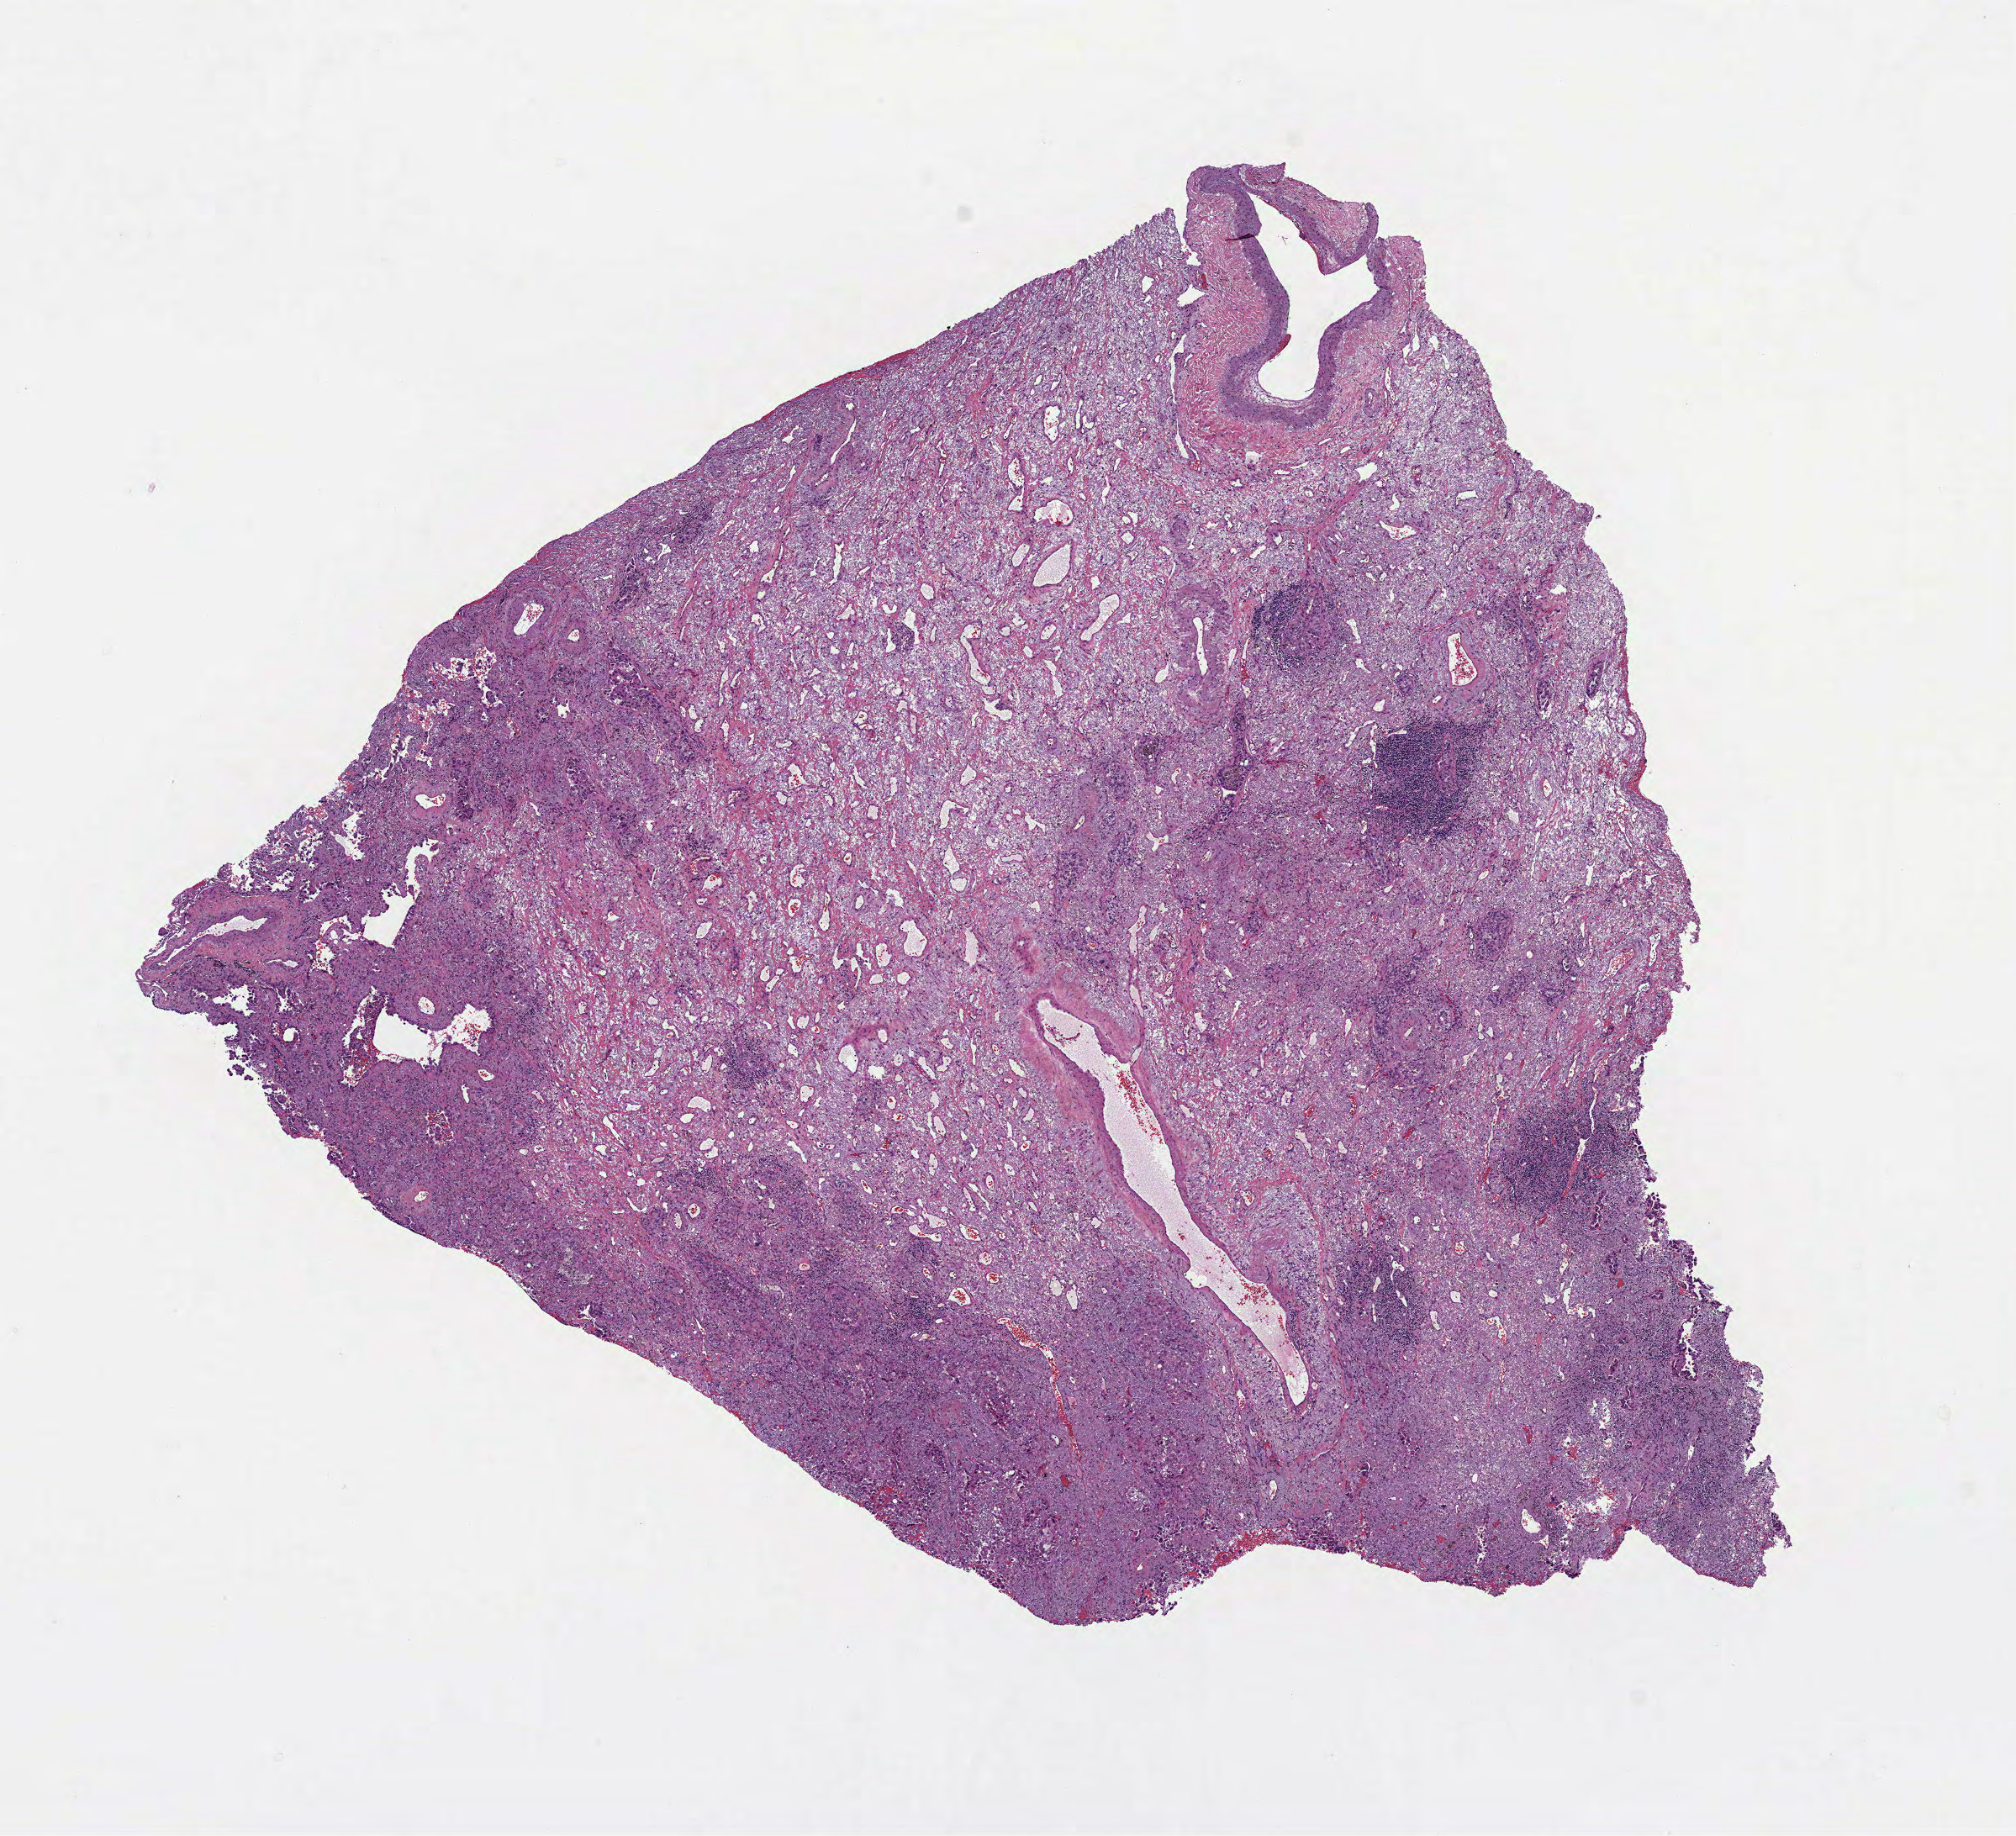
Whole-slide histology image, H&E-stained, a low-resolution overview of the entire scanned area, about 9.7 x 8.8 mm (acquisition: 40x scan). Formalin-fixed paraffin-embedded (FFPE) diagnostic section. Primary tumour sample from the lung. Female patient; age at initial diagnosis 80 years.
AJCC pathologic stage: IA (7th edition). TNM: T1b N0 M0. Diagnosis: Adenocarcinoma with mixed subtypes (upper lobe, lung).